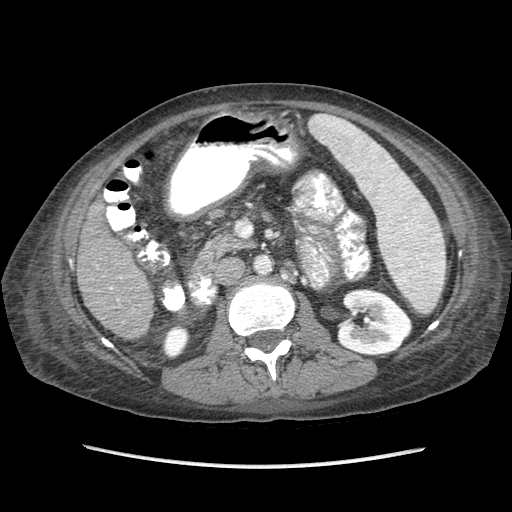
Contrast-enhanced abdominal CT (liver protocol), one axial slice; position 26 of 87 along the scan axis; reconstruction kernel STANDARD; soft-tissue window (W 400 / L 40 HU); 512 × 512 image matrix, field of view 340 × 340 mm. Case-level facts recorded for this patient, not image findings: diagnosis: hepatocellular carcinoma (patient treated with transarterial chemoembolisation; whether this scan precedes or follows treatment is not stated here); TNM stage (as recorded): Stage-IIIB; Child-Pugh class: A; tumour differentiation: no biopsy; tumour nodularity: uninodular.
Outlined on this slice (semi-automatic segmentation, software-assisted and operator-edited):
- liver parenchyma outside the tumour (the mass and vessels are separate outlines, so this box may not span the whole liver): bounding box (x1, y1, x2, y2) in pixels: (76, 197, 153, 338)
- liver vessels: (110, 287, 119, 301)